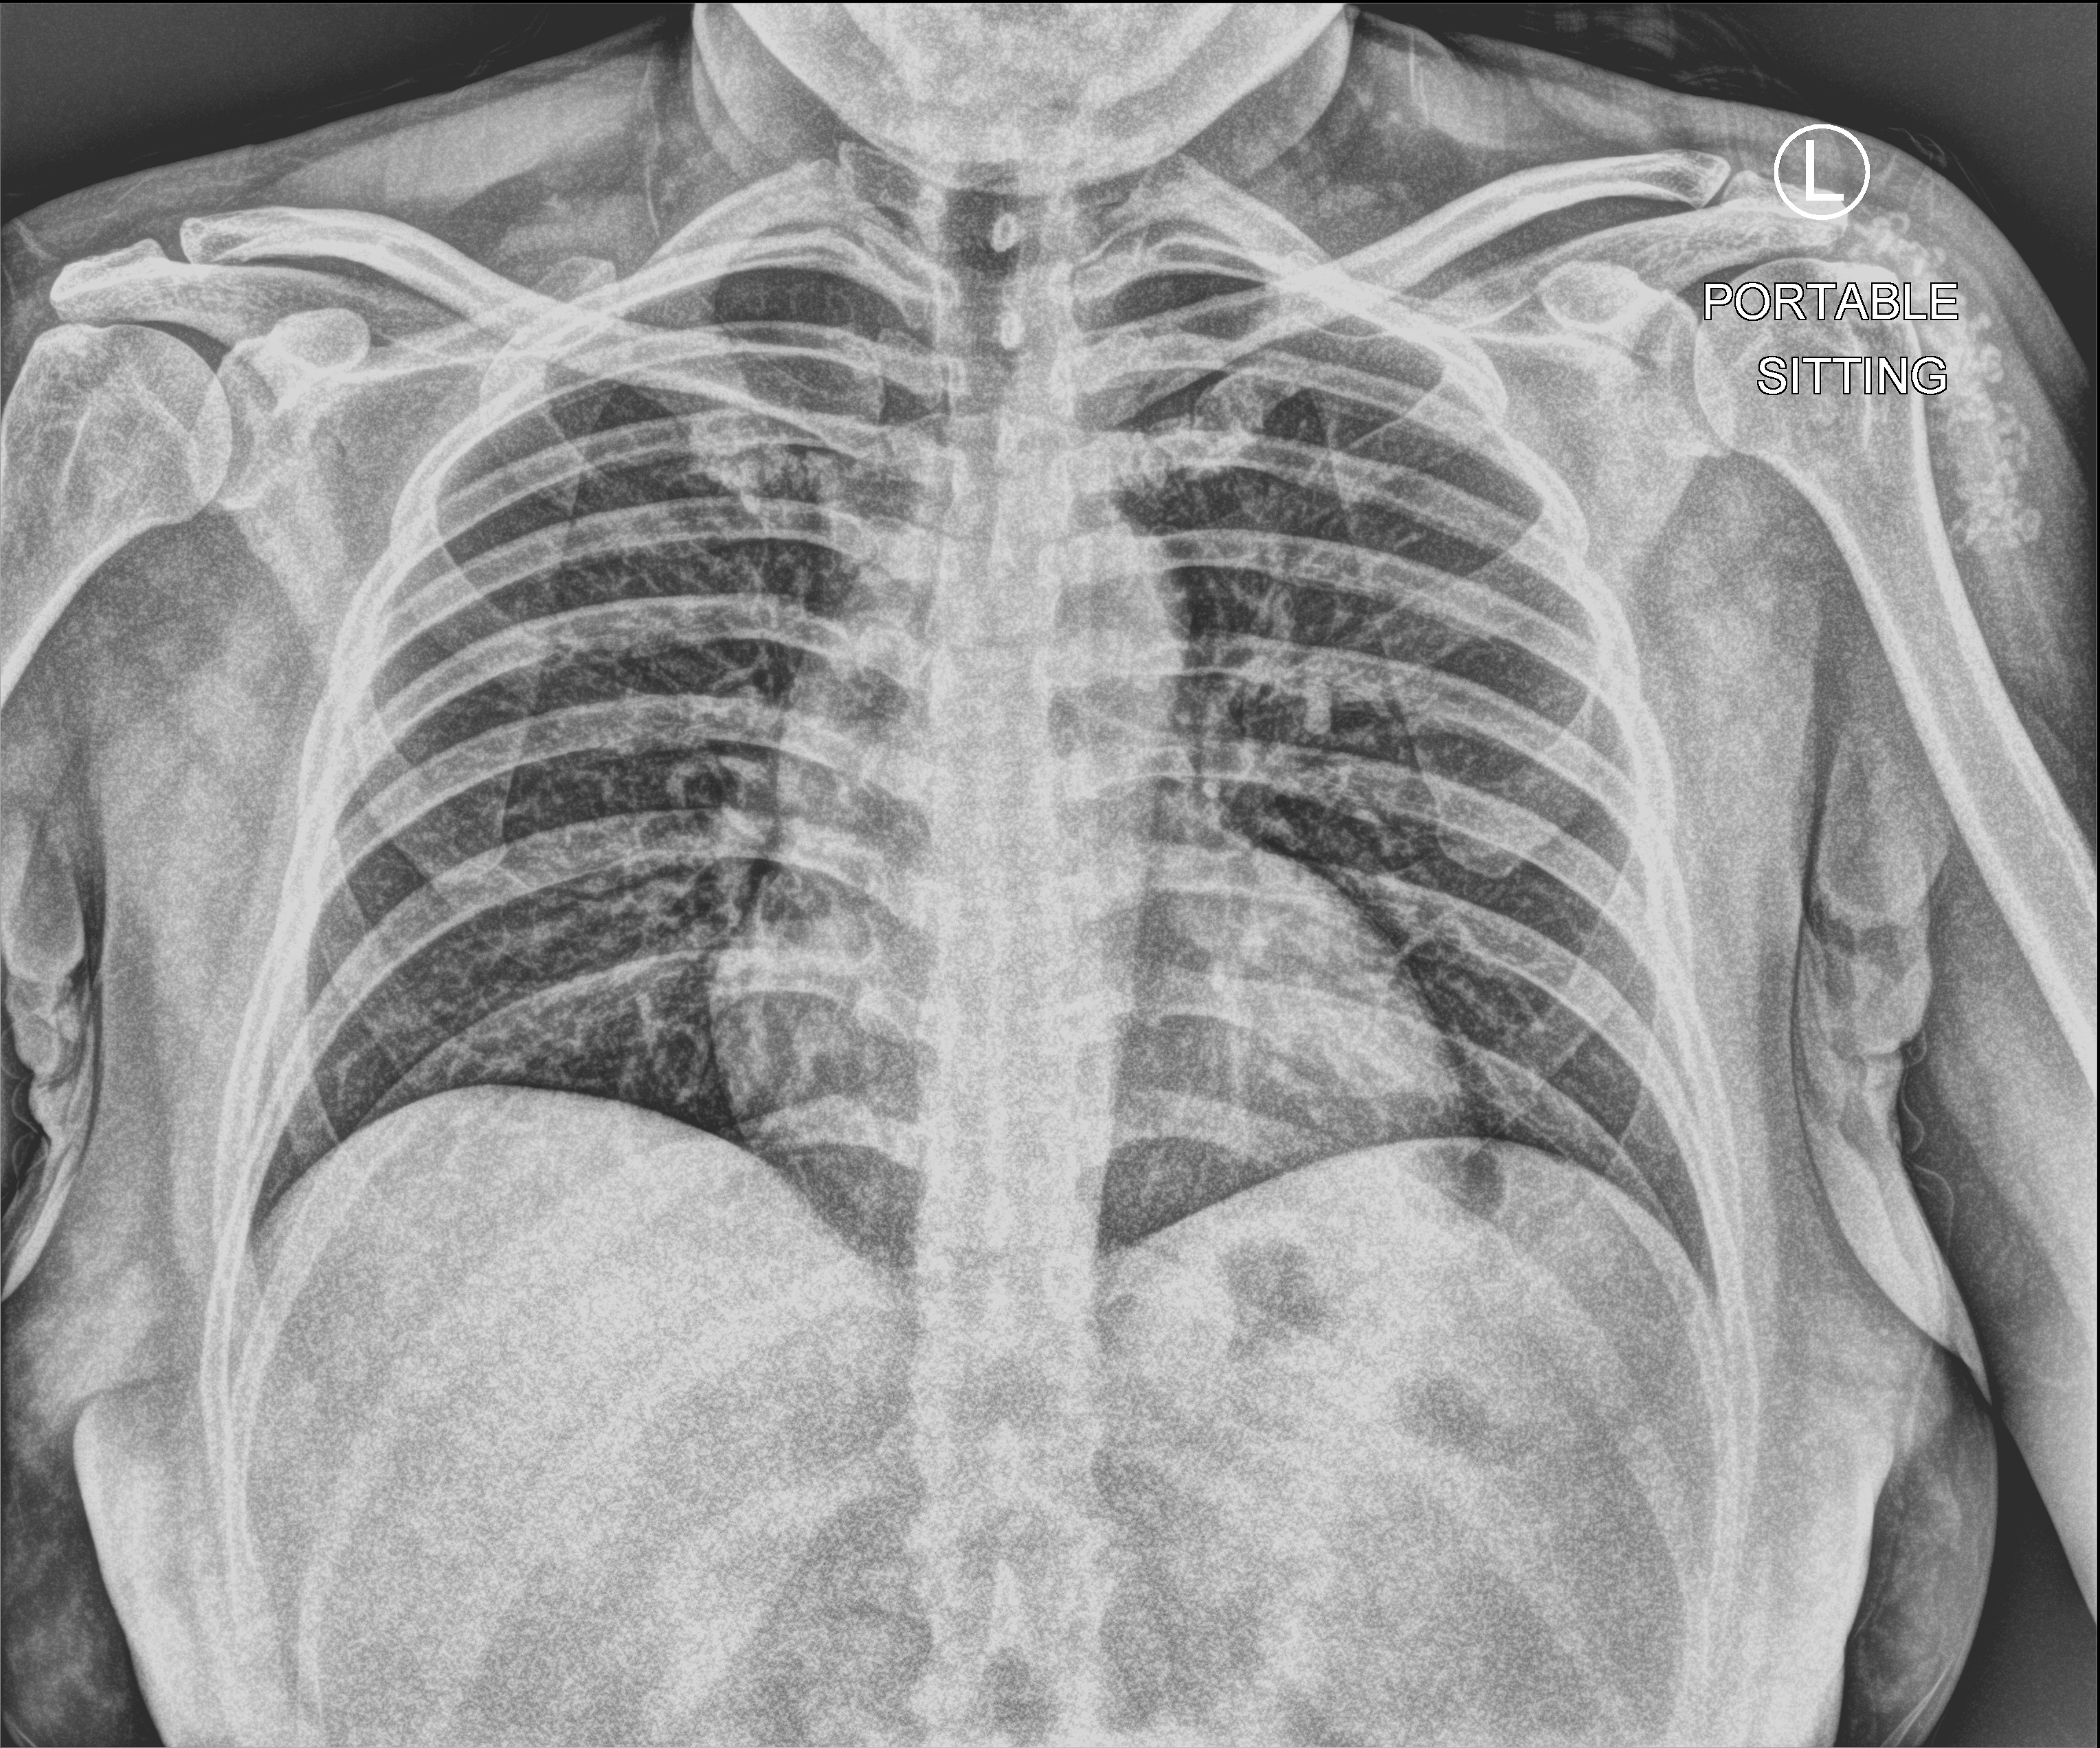
Chest X-ray (portable); anteroposterior (AP) projection. Patient hospitalised with COVID-19; female, aged 18–59 years.
From the hospital-stay record, not from the radiograph (when in the stay this image was taken is not recorded):
- admitted to intensive care during this hospital stay: no
- mechanically ventilated during this hospital stay: no